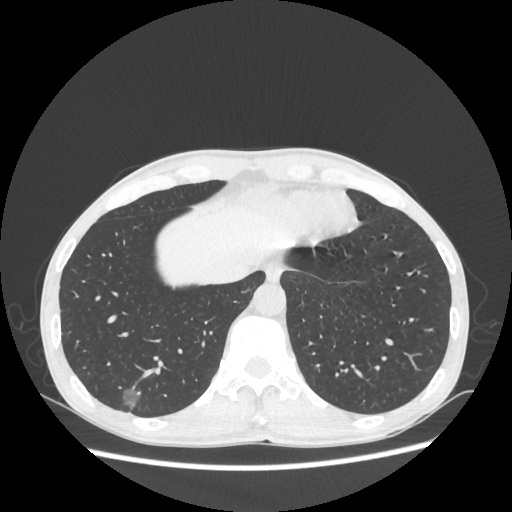
Chest CT, one axial slice; position 64 of 270 along the scan axis; reconstruction kernel STANDARD; lung window (W 1500 / L -600 HU); 512 × 512 image matrix, field of view 360 × 360 mm. Male patient, age 60 years. From the clinical record (not read from this slice): clinical TNM (as recorded): T1c N0 M0.
Outlined on this slice (rectangle marked by the reading radiologist):
- lung tumour (recorded histology: adenocarcinoma): box from (x=114, y=376) to (x=148, y=421) px